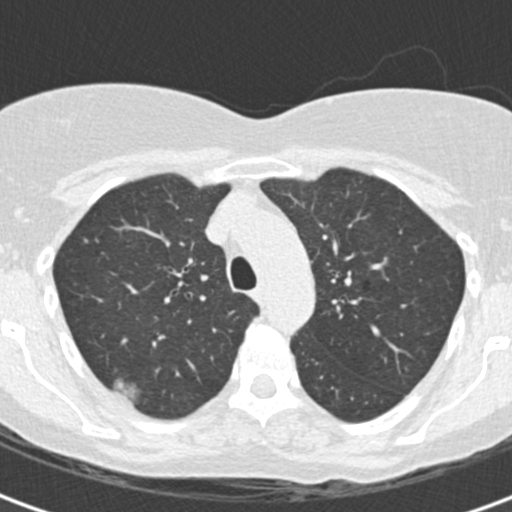
Low-dose screening chest CT, one axial slice; position 129 of 172 along the scan axis; reconstruction kernel B30f; 120 kVp; lung window (W 1500 / L -600 HU); 2 mm slice thickness; 512 × 512 image matrix, field of view 283 × 283 mm.
Structures marked on this image (expert manual segmentation):
- lesion 1 (tumor, upper lobe of right lung): box from (x=113, y=377) to (x=142, y=403) px